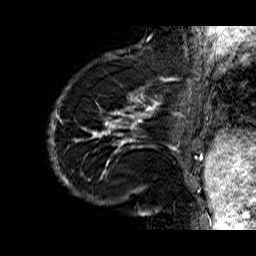
Breast MRI (dynamic contrast-enhanced), one sagittal slice; slice 8 of 60 in the series (ordered by position); dynamic contrast-enhanced series, time point 2 of 6 at this slice position (early post-contrast); 1.5 T; TE 6.3 ms, TR 32.9 ms; 4 mm slice thickness; 256 × 256 image matrix, field of view 200 × 200 mm. Female patient. Case-level facts recorded for this patient, not image findings: setting: breast cancer imaged before/during neoadjuvant chemotherapy; receptor status: HR-positive, HER2-negative.
Annotated regions visible in this slice (semi-automatic segmentation, software-assisted and operator-edited):
- analysis volume of interest (the breast-tissue region the enhancement analysis was run in; not a lesion): bounding box <48,74,176,210> (left, top, right, bottom; pixels)
- tumour enhancement mask (voxels above the 100 % enhancement threshold inside the analysis volume of interest): <49,78,173,210>